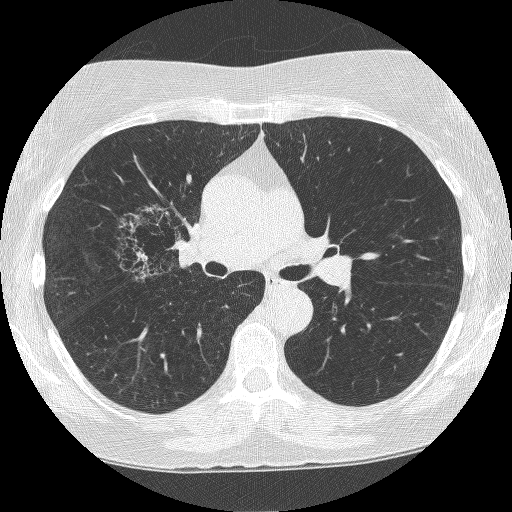
Axial slice from a low-dose chest CT screening exam; second annual screen; lung window (W 1500 / L -600 HU). Female participant, aged 64 years at enrolment. Former smoker at enrolment.
- Expert reader's lesion annotation, bounding box (x1, y1, x2, y2) in pixels: (116, 205, 203, 288).
- The screening reader recorded 4 non-calcified nodules or masses ≥4 mm on this exam (right upper lobe, right upper lobe, right upper lobe, left upper lobe); which of them this box marks is not recorded.
- Participant outcome: lung cancer diagnosed 381 days after this screen — adenocarcinoma, NOS, right upper lobe, right middle lobe, right hilum, stage IV (AJCC 6th edition), 85 mm at pathology.